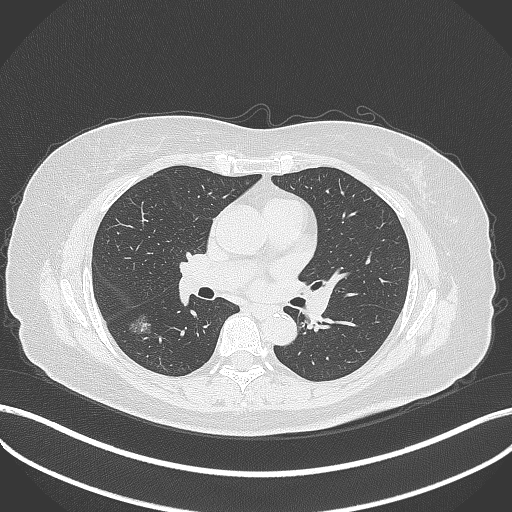
Chest CT, one axial slice. Slice 172 of 322 in the series (ordered by position). Reconstruction kernel B70f. 120 kVp. Lung window (W 1500 / L -600 HU). 512 × 512 image matrix, field of view 400 × 400 mm. Female patient, age 64 years. Case-level facts recorded for this patient, not image findings: clinical TNM (as recorded): T1c N0 M0; histopathological grade: G1.
Outlined on this slice (rectangle marked by the reading radiologist):
- lung tumour (recorded histology: adenocarcinoma): box from (x=127, y=311) to (x=155, y=342) px